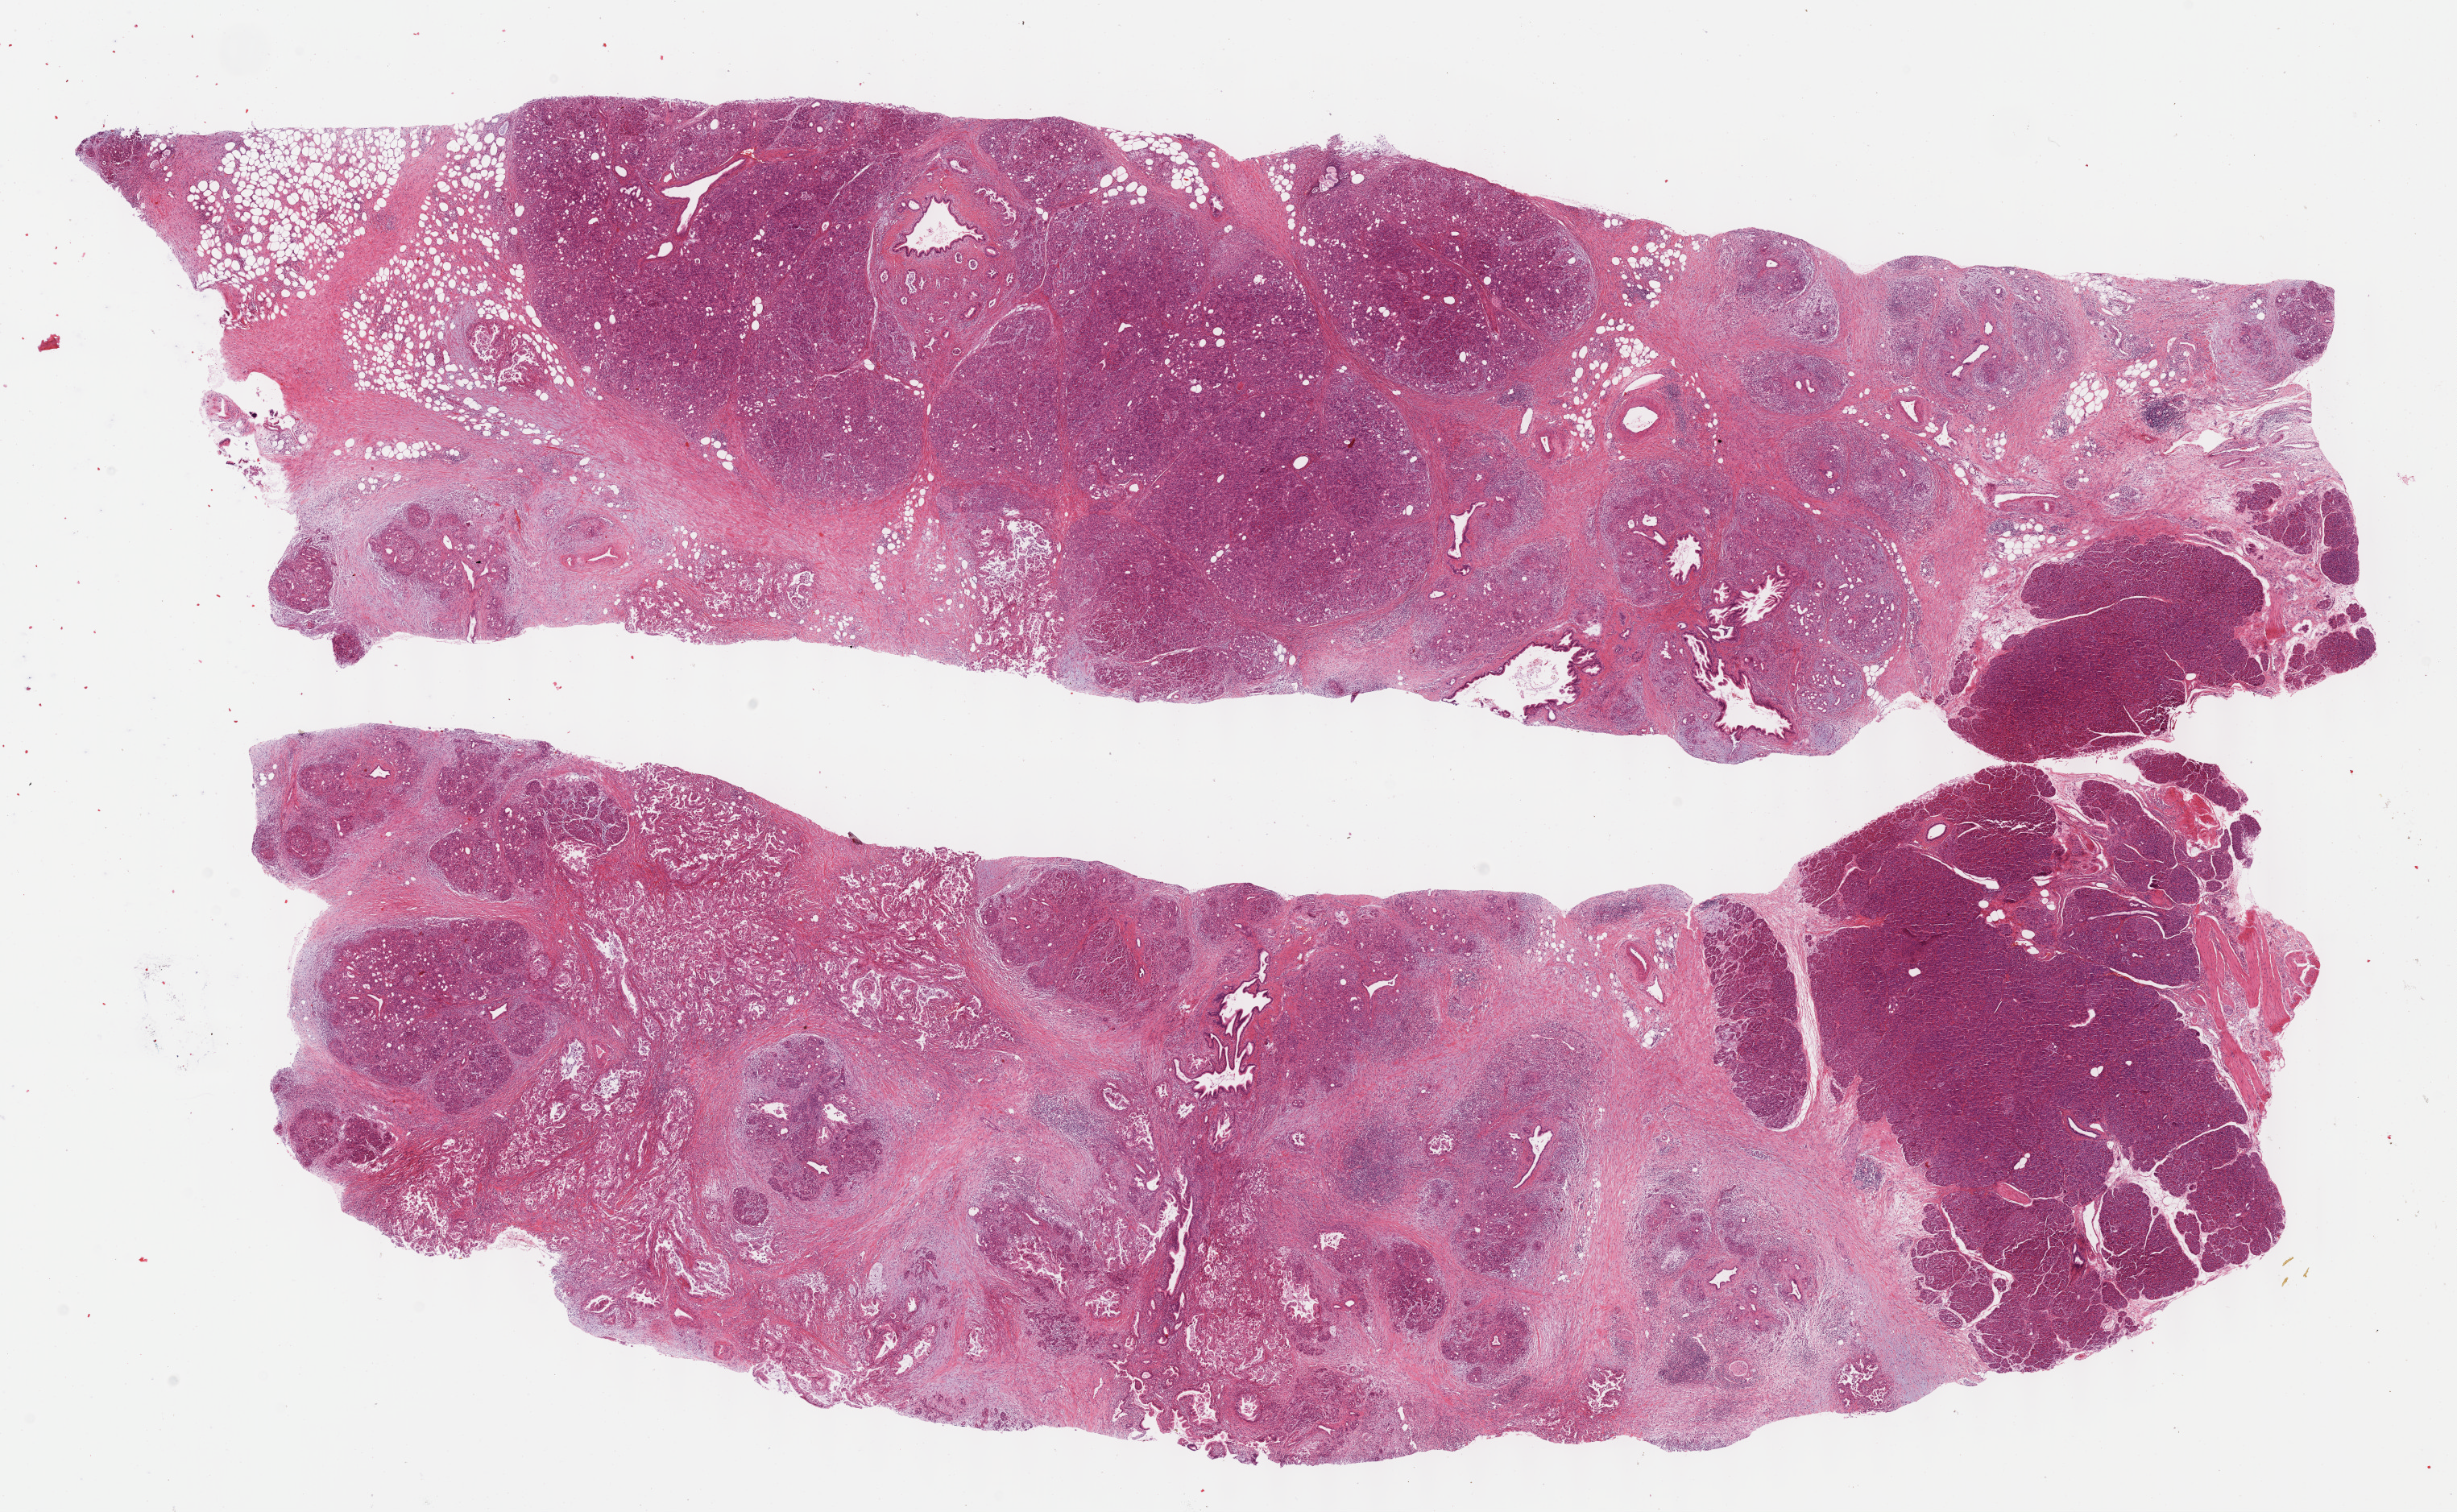
H&E whole-slide image — low-resolution overview of the scanned area, about 24.6 x 15.2 mm. Formalin-fixed paraffin-embedded (FFPE) diagnostic section. Primary tumour sample from the pancreas. Male patient; age at initial diagnosis 50 years. Histologic grade: G3 (poorly differentiated).
* AJCC pathologic stage: IIB (7th edition)
* lymph nodes positive (case pathology): 3 of 20 examined
* TNM: T3 N1 MX
* pathologic diagnosis: Infiltrating duct carcinoma, NOS (head of pancreas)